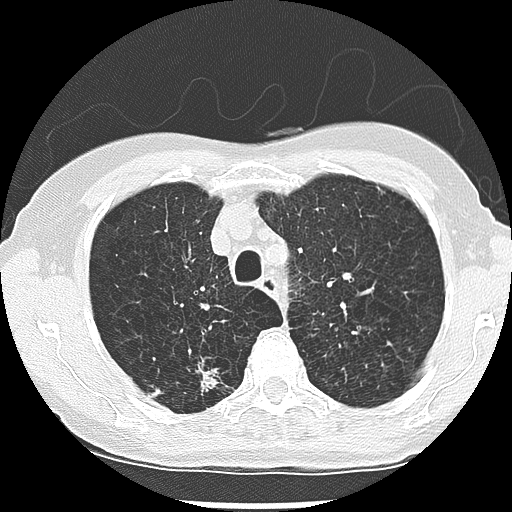
Low-dose screening chest CT, one axial slice. Slice 212 of 265 in the series (ordered by position). Reconstruction kernel LUNG. 120 kVp. Lung window (W 1500 / L -600 HU). 2.5 mm slice thickness. 512 × 512 image matrix, field of view 300 × 300 mm.
Structures marked on this image (expert manual segmentation):
- lesion 1 (nodule, upper lobe of right lung): box from (x=201, y=369) to (x=218, y=391) px